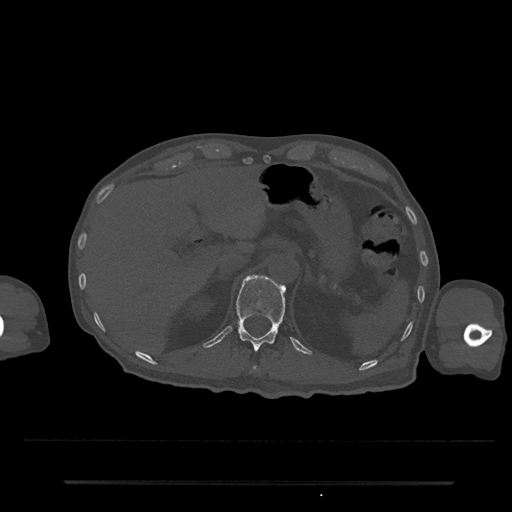
CT including the spine, one axial slice. Position 194 of 797 along the scan axis. Reconstruction kernel Br40s/3. 120 kVp. Bone window (W 1800 / L 400 HU). 0.5 mm slice thickness. 512 × 512 image matrix, field of view 427 × 427 mm. Patient: male, 74 years. Case-level facts recorded for this patient, not image findings: primary cancer: prostate.
Outlined on this slice (semi-automatically segmented with operator editing):
- T11 vertebra: bounding box [x1, y1, x2, y2] px = [252, 366, 259, 373]
- T12 vertebra: [236, 276, 285, 351]